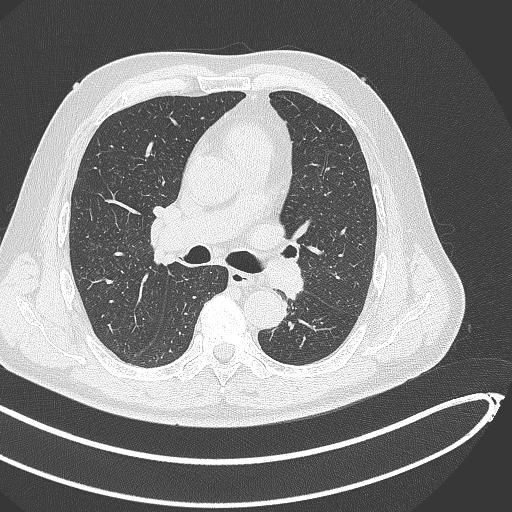
Chest CT, one axial slice; lung window (W 1500 / L -600 HU); 1 mm slice thickness; 512 × 512 image matrix. Patient: male, 64 years. Case-level facts recorded for this patient, not image findings: clinical TNM (as recorded): T1c N0 M0.
Annotated regions visible in this slice (rectangle marked by the reading radiologist):
- lung tumour (recorded histology: squamous cell carcinoma): bounding box (x1, y1, x2, y2) in pixels: (265, 251, 307, 303)